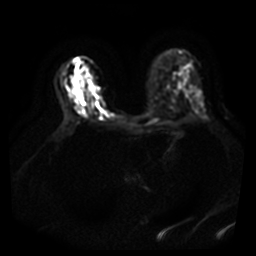
Breast MRI, one axial slice; position 25 of 40 along the scan axis; diffusion-weighted series; image 2 of 4 stored at this slice position (different b-values; order by instance number); 3 T; 256 × 256 image matrix, field of view 380 × 380 mm. Female patient.
Annotated regions visible in this slice (expert manual segmentation):
- tumour on diffusion-weighted imaging: bounding box (x1, y1, x2, y2) in pixels: (79, 109, 87, 118)